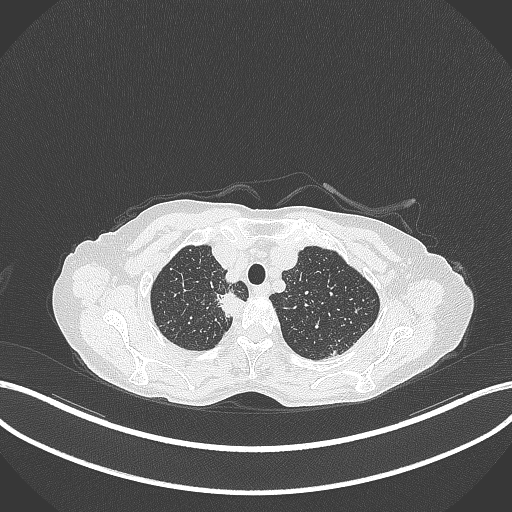
Chest CT, one axial slice; slice 317 of 403 in the series (ordered by position); reconstruction kernel B70f; 120 kVp; lung window (W 1500 / L -600 HU); 512 × 512 image matrix. Female patient, age 75 years. Case-level facts recorded for this patient, not image findings: clinical TNM (as recorded): T1c N1 M1.
Annotated regions visible in this slice (rectangle marked by the reading radiologist):
- lung tumour (recorded histology: adenocarcinoma): bounding box [x1, y1, x2, y2] px = [212, 289, 250, 320]